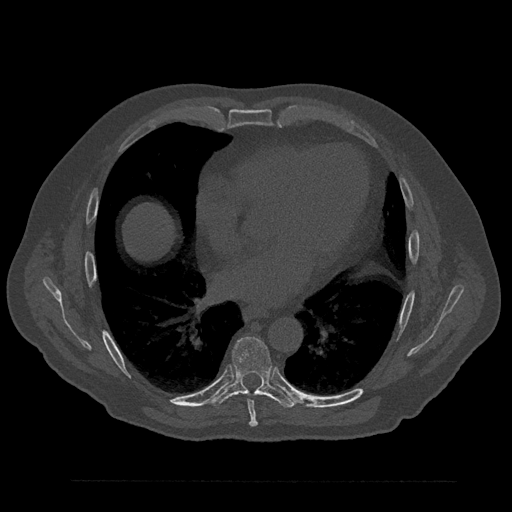
CT including the spine, one axial slice. Position 472 of 797 along the scan axis. Reconstruction kernel Br40s/3. 120 kVp. Bone window (W 1800 / L 400 HU). 512 × 512 image matrix, field of view 430 × 430 mm. Male patient, age 61 years. From the clinical record (not read from this slice): primary cancer: prostate.
Outlined on this slice (semi-automatically segmented with operator editing):
- T7 vertebra: bounding box (x1, y1, x2, y2) in pixels: (243, 393, 258, 427)
- T8 vertebra: (211, 336, 296, 408)